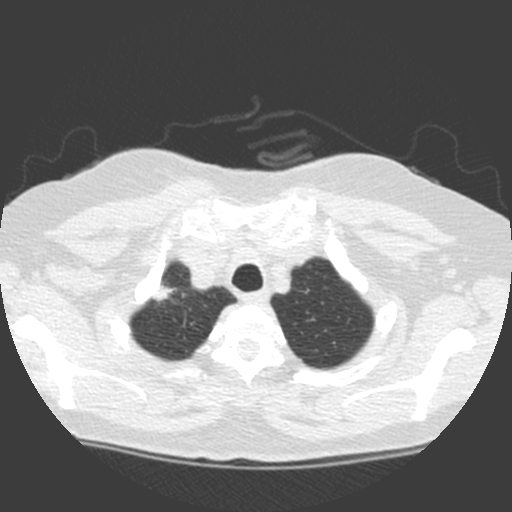
Low-dose screening chest CT, one axial slice. Slice 143 of 155 in the series (ordered by position). 120 kVp. Lung window (W 1500 / L -600 HU). 2 mm slice thickness. 512 × 512 image matrix, field of view 314 × 314 mm.
Structures marked on this image (outlined manually by an expert reader):
- lesion 1 (tumor, upper lobe of right lung): bounding box (x1, y1, x2, y2) in pixels: (152, 284, 176, 302)